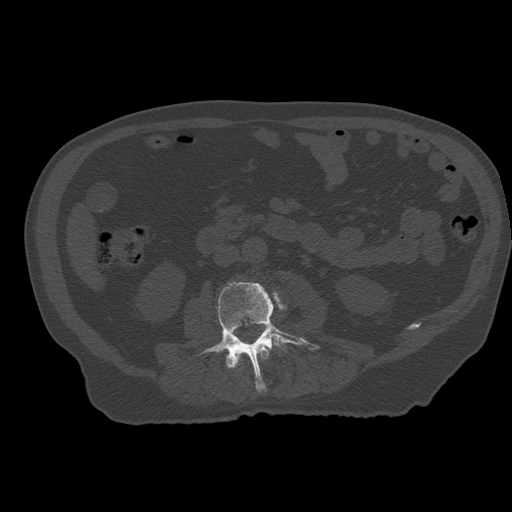
CT including the spine, one axial slice; position 190 of 399 along the scan axis; reconstruction kernel STANDARD; 120 kVp; bone window (W 1800 / L 400 HU); 1.25 mm slice thickness; 512 × 512 image matrix. Patient age 73 years. Case-level facts recorded for this patient, not image findings: primary cancer: prostate.
Structures marked on this image (semi-automatic segmentation, software-assisted and operator-edited):
- L2 vertebra: bounding box [x1, y1, x2, y2] px = [232, 343, 270, 368]
- L3 vertebra: [200, 282, 319, 392]